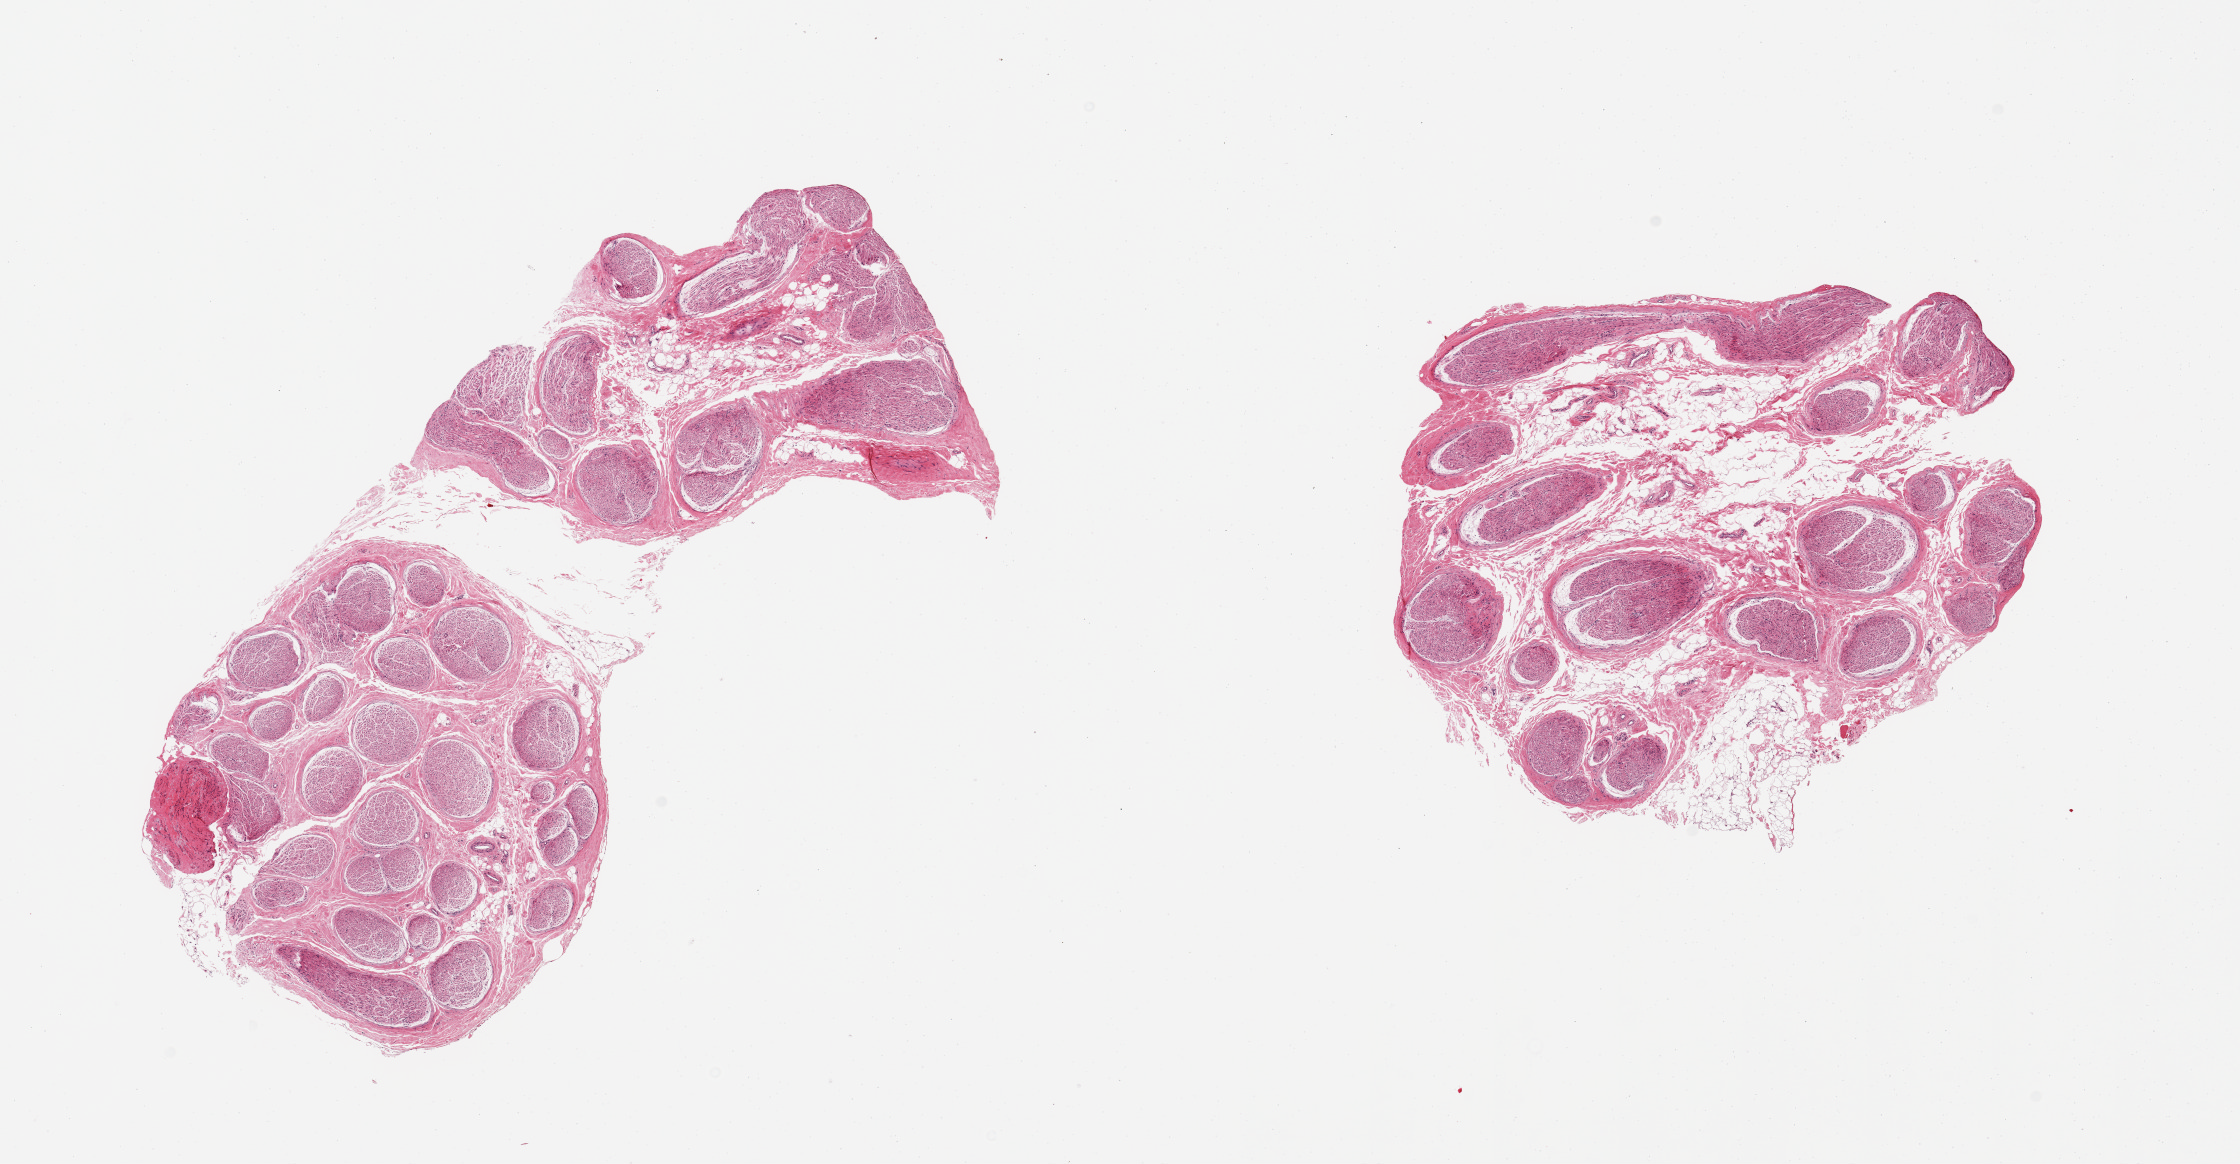
Haematoxylin and eosin whole-slide image, whole scanned area (about 17.7 x 9.2 mm) shown as a low-resolution overview, PAXgene-fixed, paraffin-embedded tissue, sampled site (target tissue): tibial nerve, donor tissue sample.
Reviewer comment on this tissue sample: 2 pieces; 10 & 50% internal fibrofatty tissue.